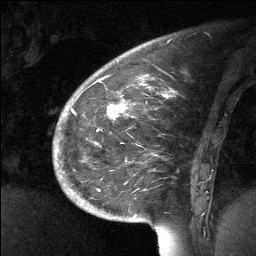
Breast MRI (dynamic contrast-enhanced), one sagittal slice; slice 19 of 64 in the series (ordered by position); dynamic contrast-enhanced study with each time point stored as its own series, time point 2 of 3 at this slice position (early post-contrast, ordered by acquisition time); 1.5 T; TE 4.8 ms, TR 27 ms; 2 mm slice thickness; 256 × 256 image matrix, field of view 200 × 200 mm. Patient: female, 39 years. From the clinical record (not read from this slice): setting: breast cancer imaged before/during neoadjuvant chemotherapy; receptor status: HER2-positive.
Structures marked on this image (semi-automatically segmented with operator editing):
- analysis volume of interest (the breast-tissue region the enhancement analysis was run in; not a lesion): bounding box <70,69,202,224> (left, top, right, bottom; pixels)
- tumour enhancement mask (voxels above the 90 % enhancement threshold inside the analysis volume of interest): <108,104,123,116>